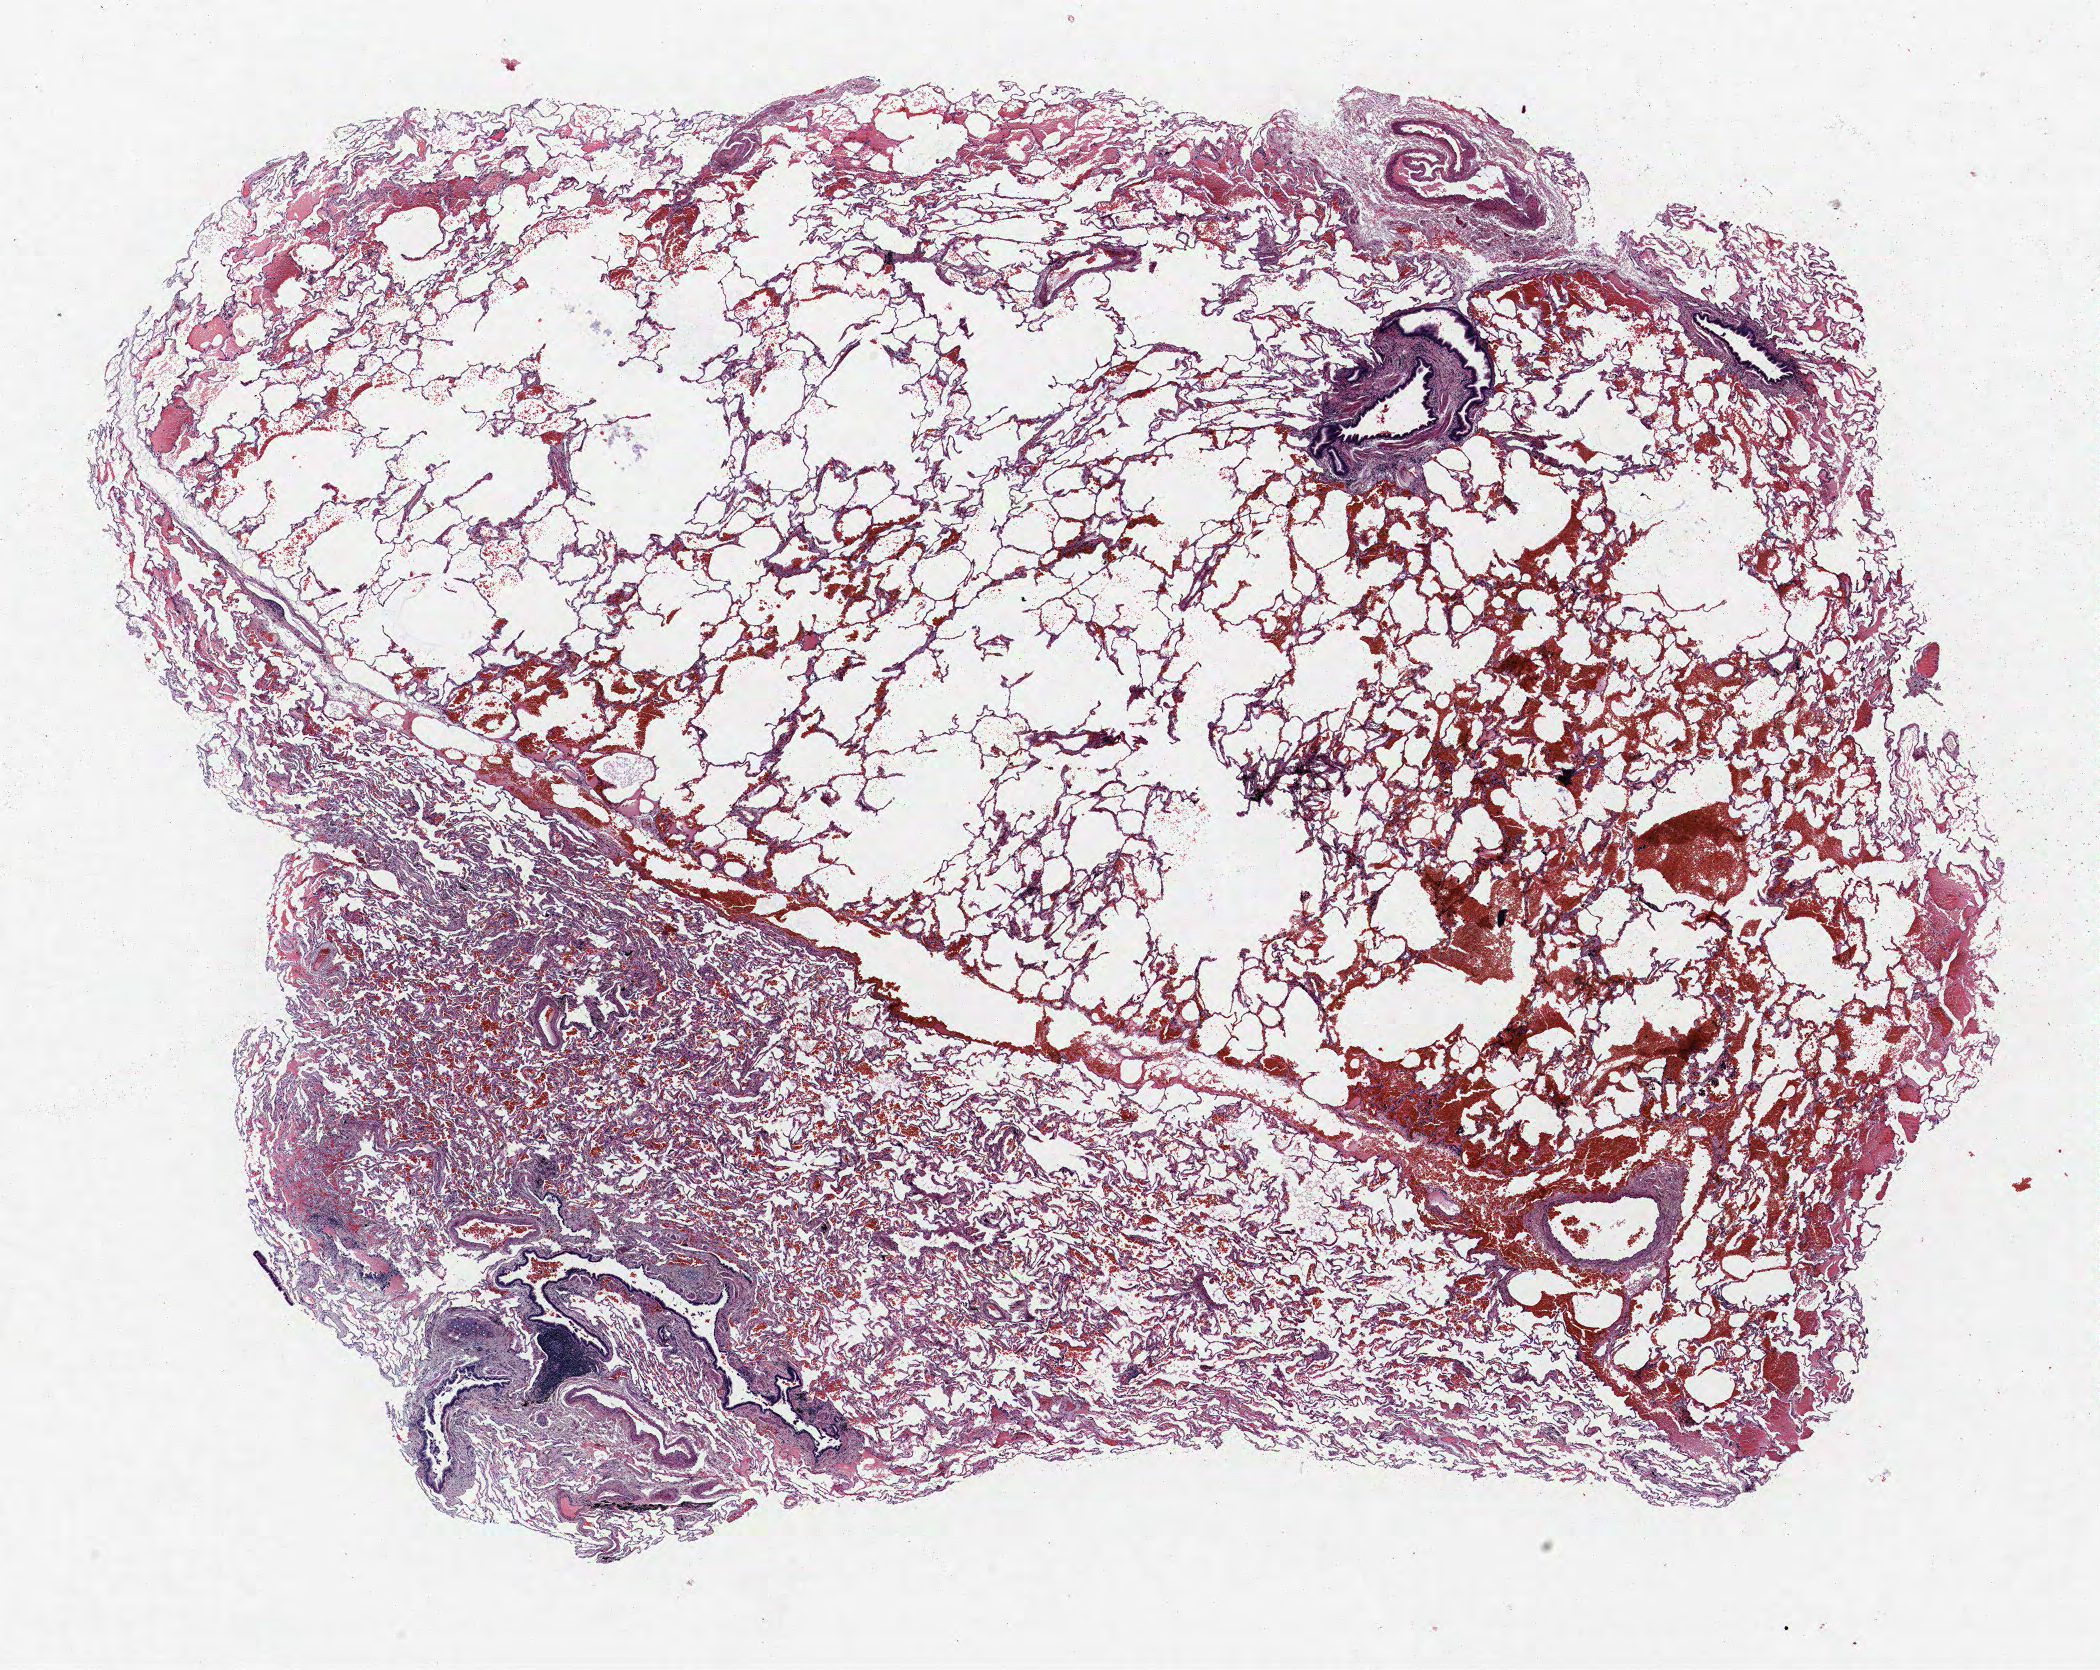
Hematoxylin and eosin (H&E) stained whole-slide image — shown as a low-resolution overview of the whole scanned area (about 16.8 x 13.4 mm, acquisition: 40x scan); formalin-fixed paraffin-embedded (FFPE) section; lung tissue. Female, age 69 at enrolment. Former smoker at enrolment. Grade: poorly differentiated (G3).
Tumour size (pathology): 36 mm. Stage (AJCC 6th edition): IB. Participant's lung-cancer diagnosis: Non-small cell carcinoma. Primary tumour location (clinical record): right lower lobe.